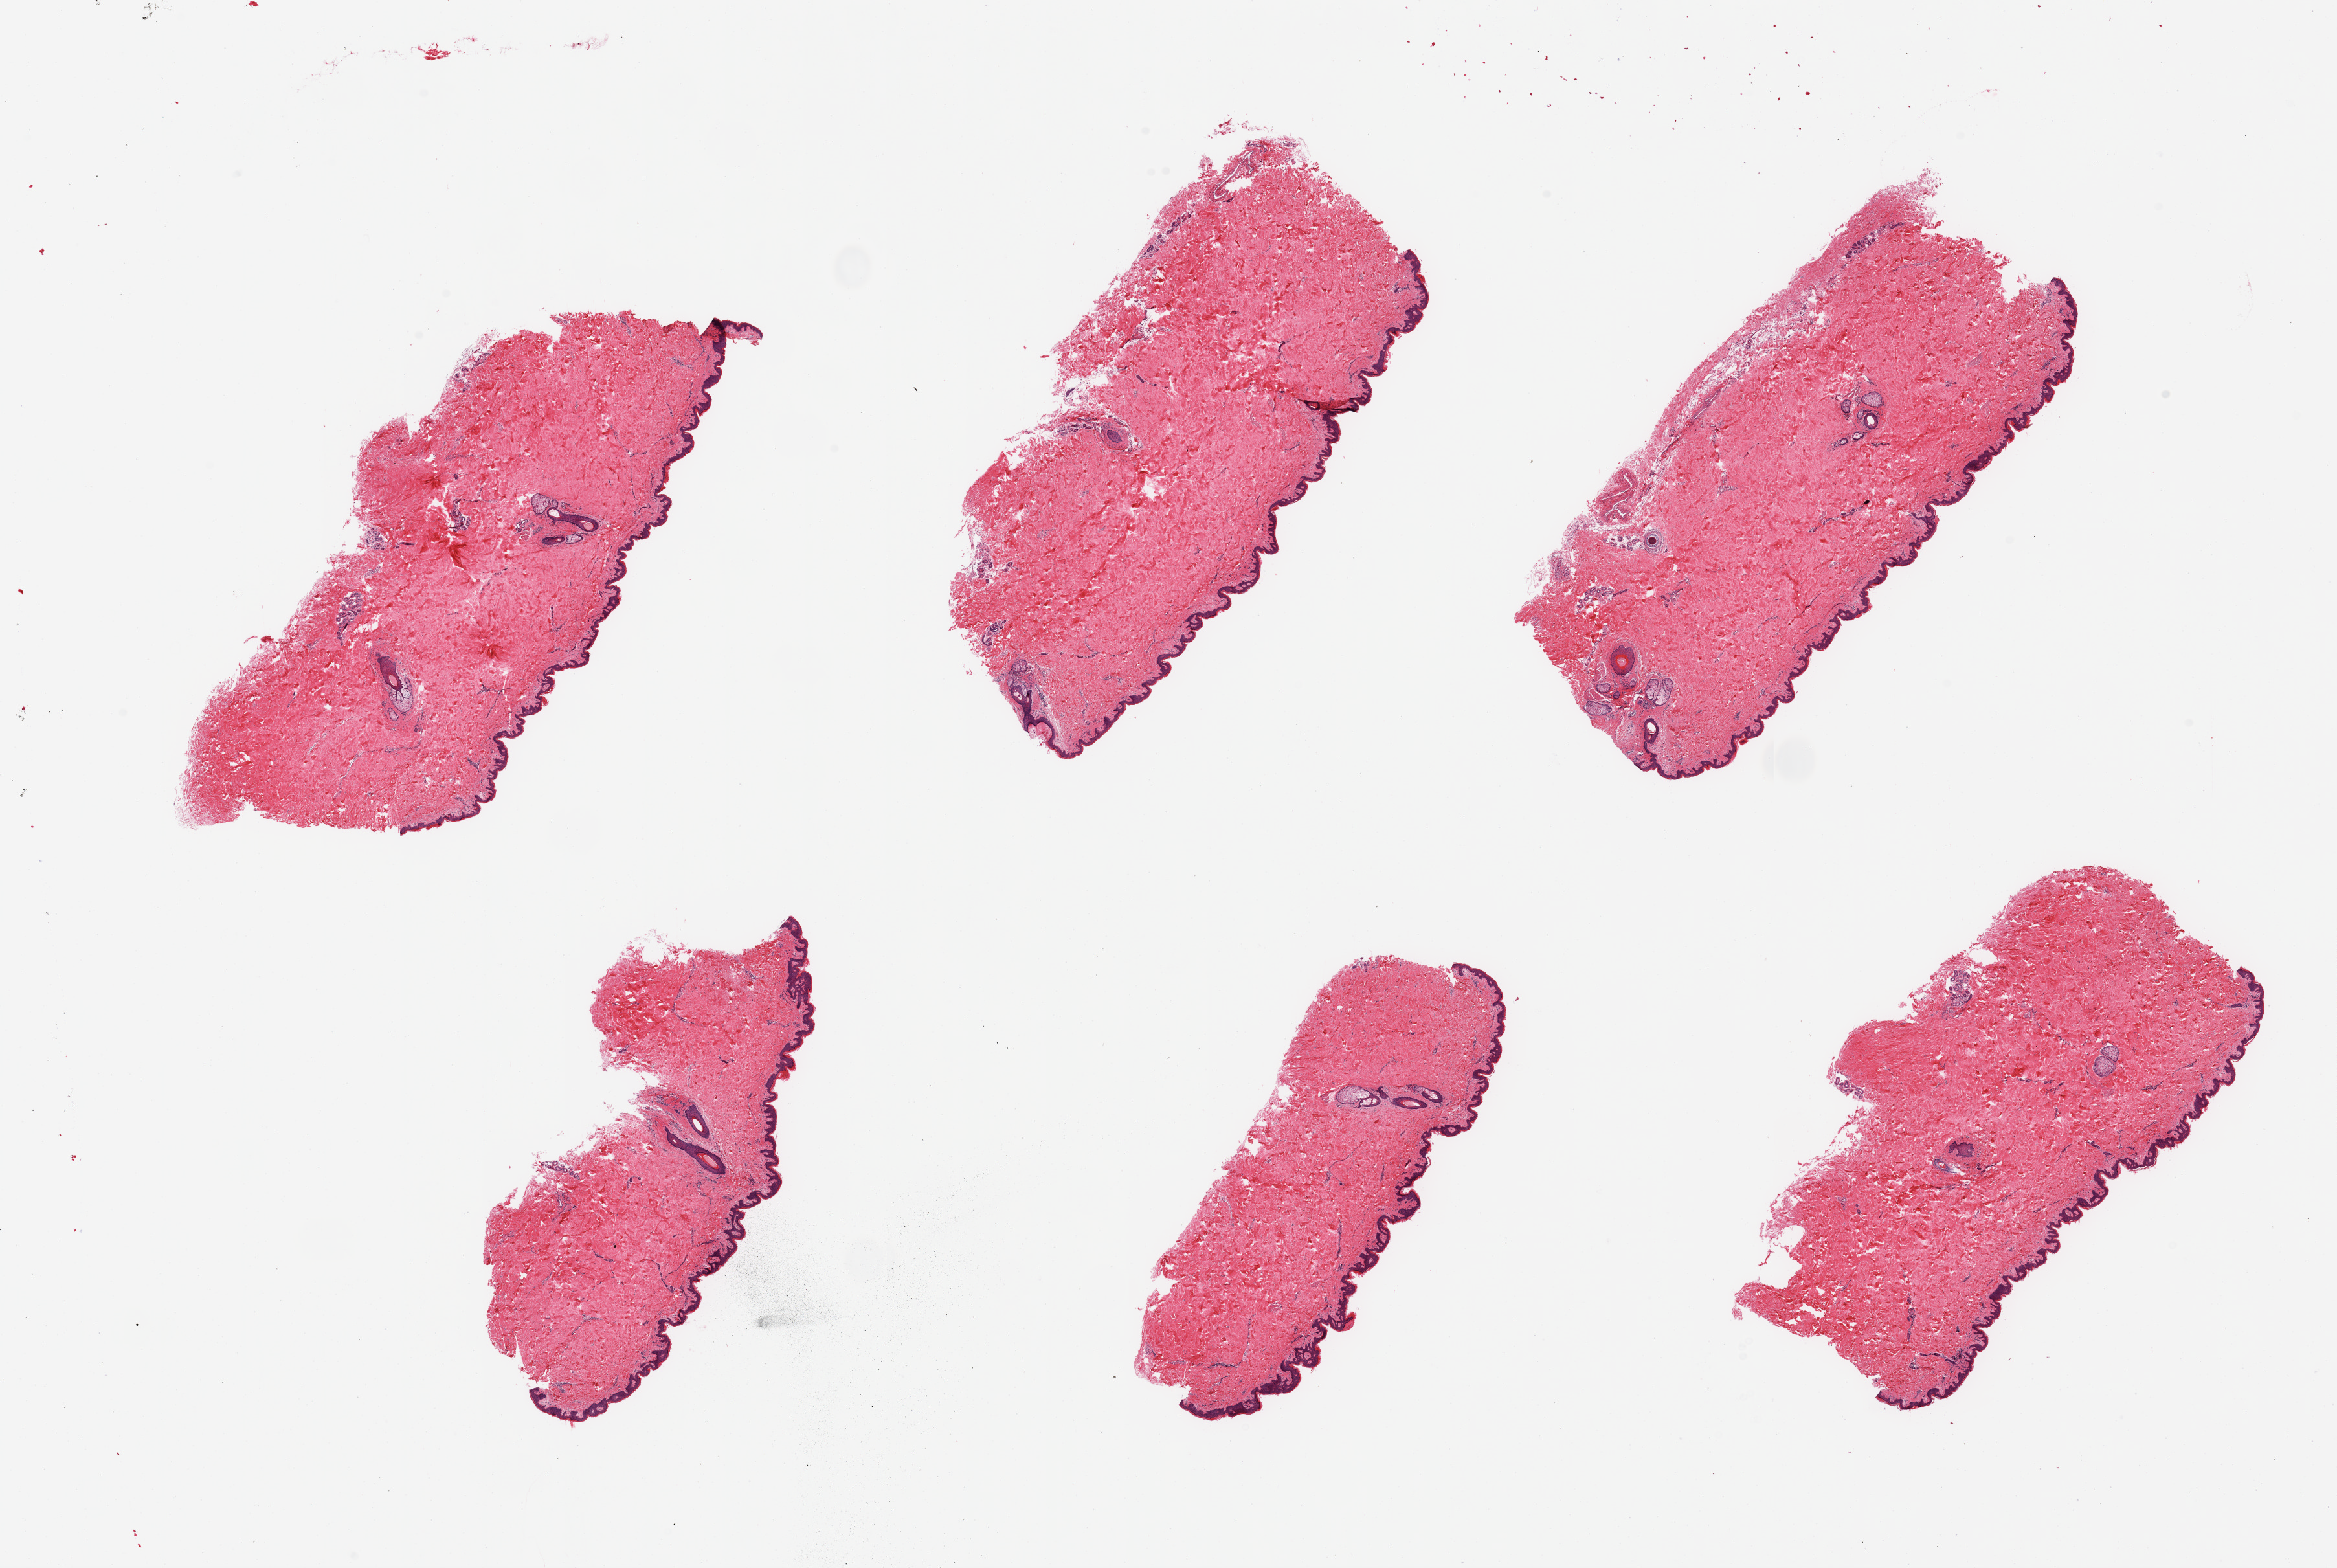
Digitized hematoxylin and eosin (H&E)-stained section, brightfield — a low-resolution overview of the entire scanned area, about 28.5 x 19.2 mm; PAXgene-fixed, paraffin-embedded tissue; section of skin of suprapubic region (target tissue); donor tissue sample. Male donor.
Review note (as recorded): 6 pieces, no significant dermal fat; squamous epithelium is 40-50 microns.